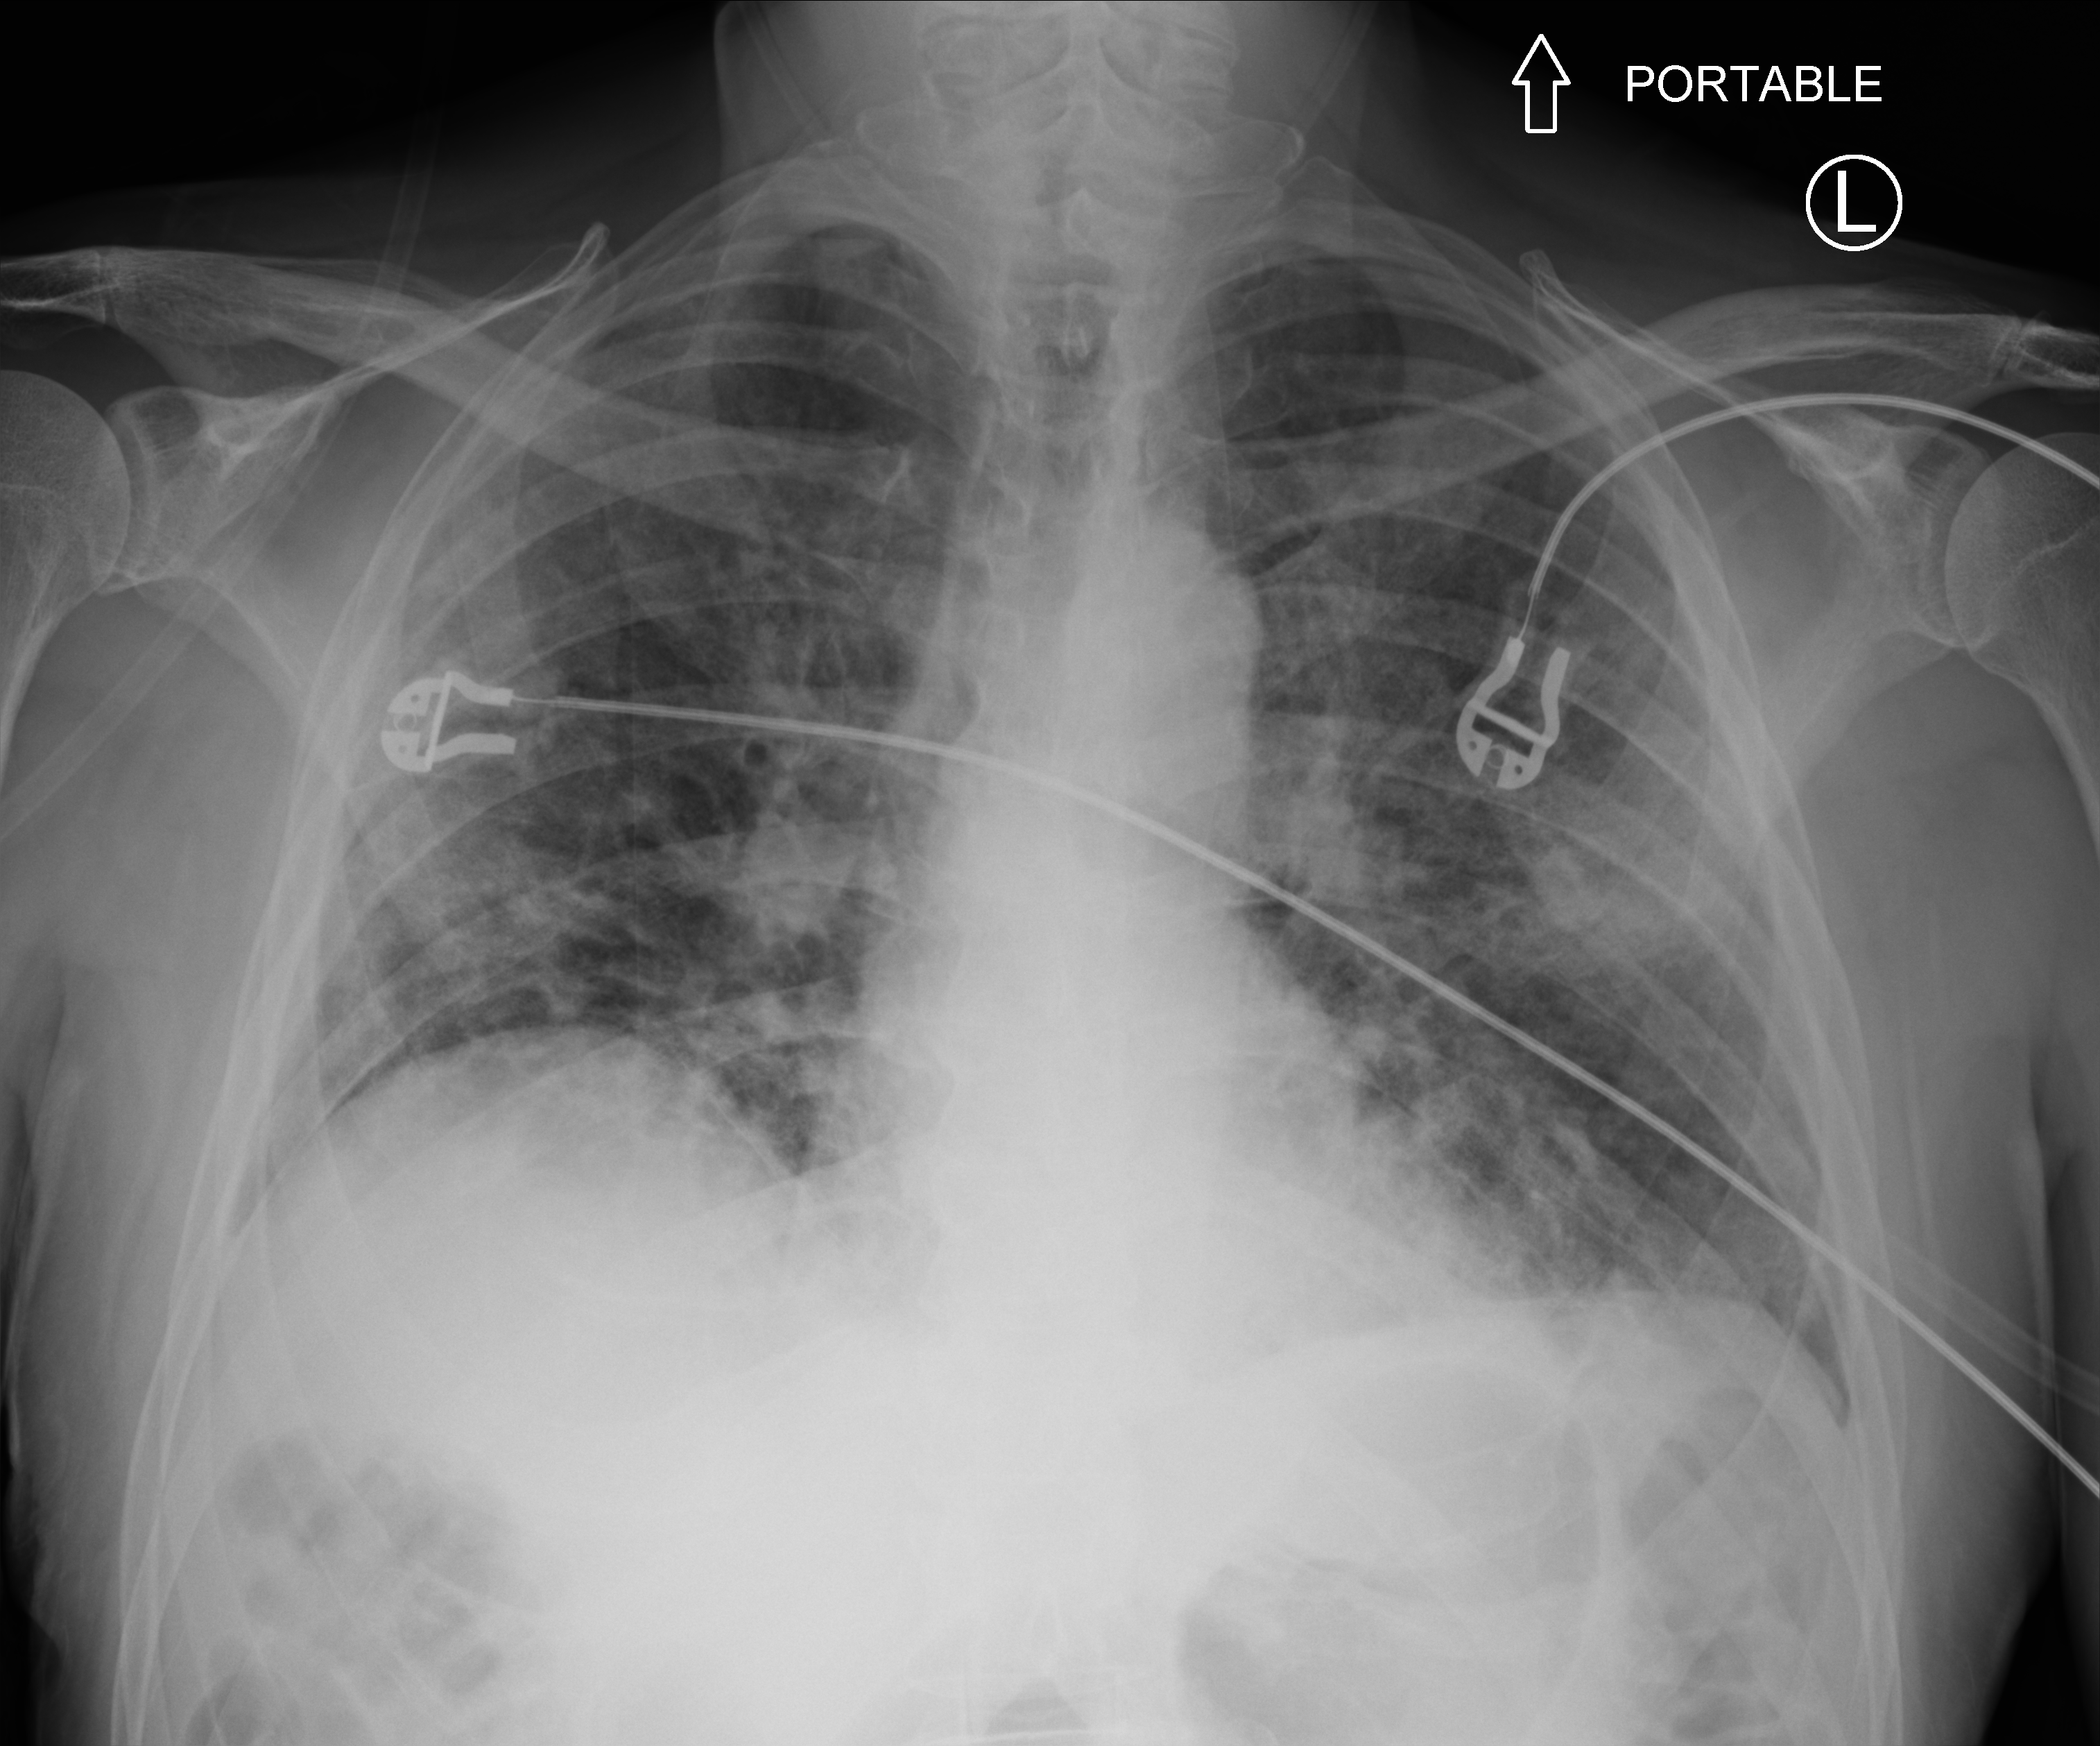
Portable chest radiograph. Male patient hospitalised with COVID-19, age 60–74 years.
From the hospital-stay record, not from the radiograph (when in the stay this image was taken is not recorded):
- length of hospital stay: 7 days